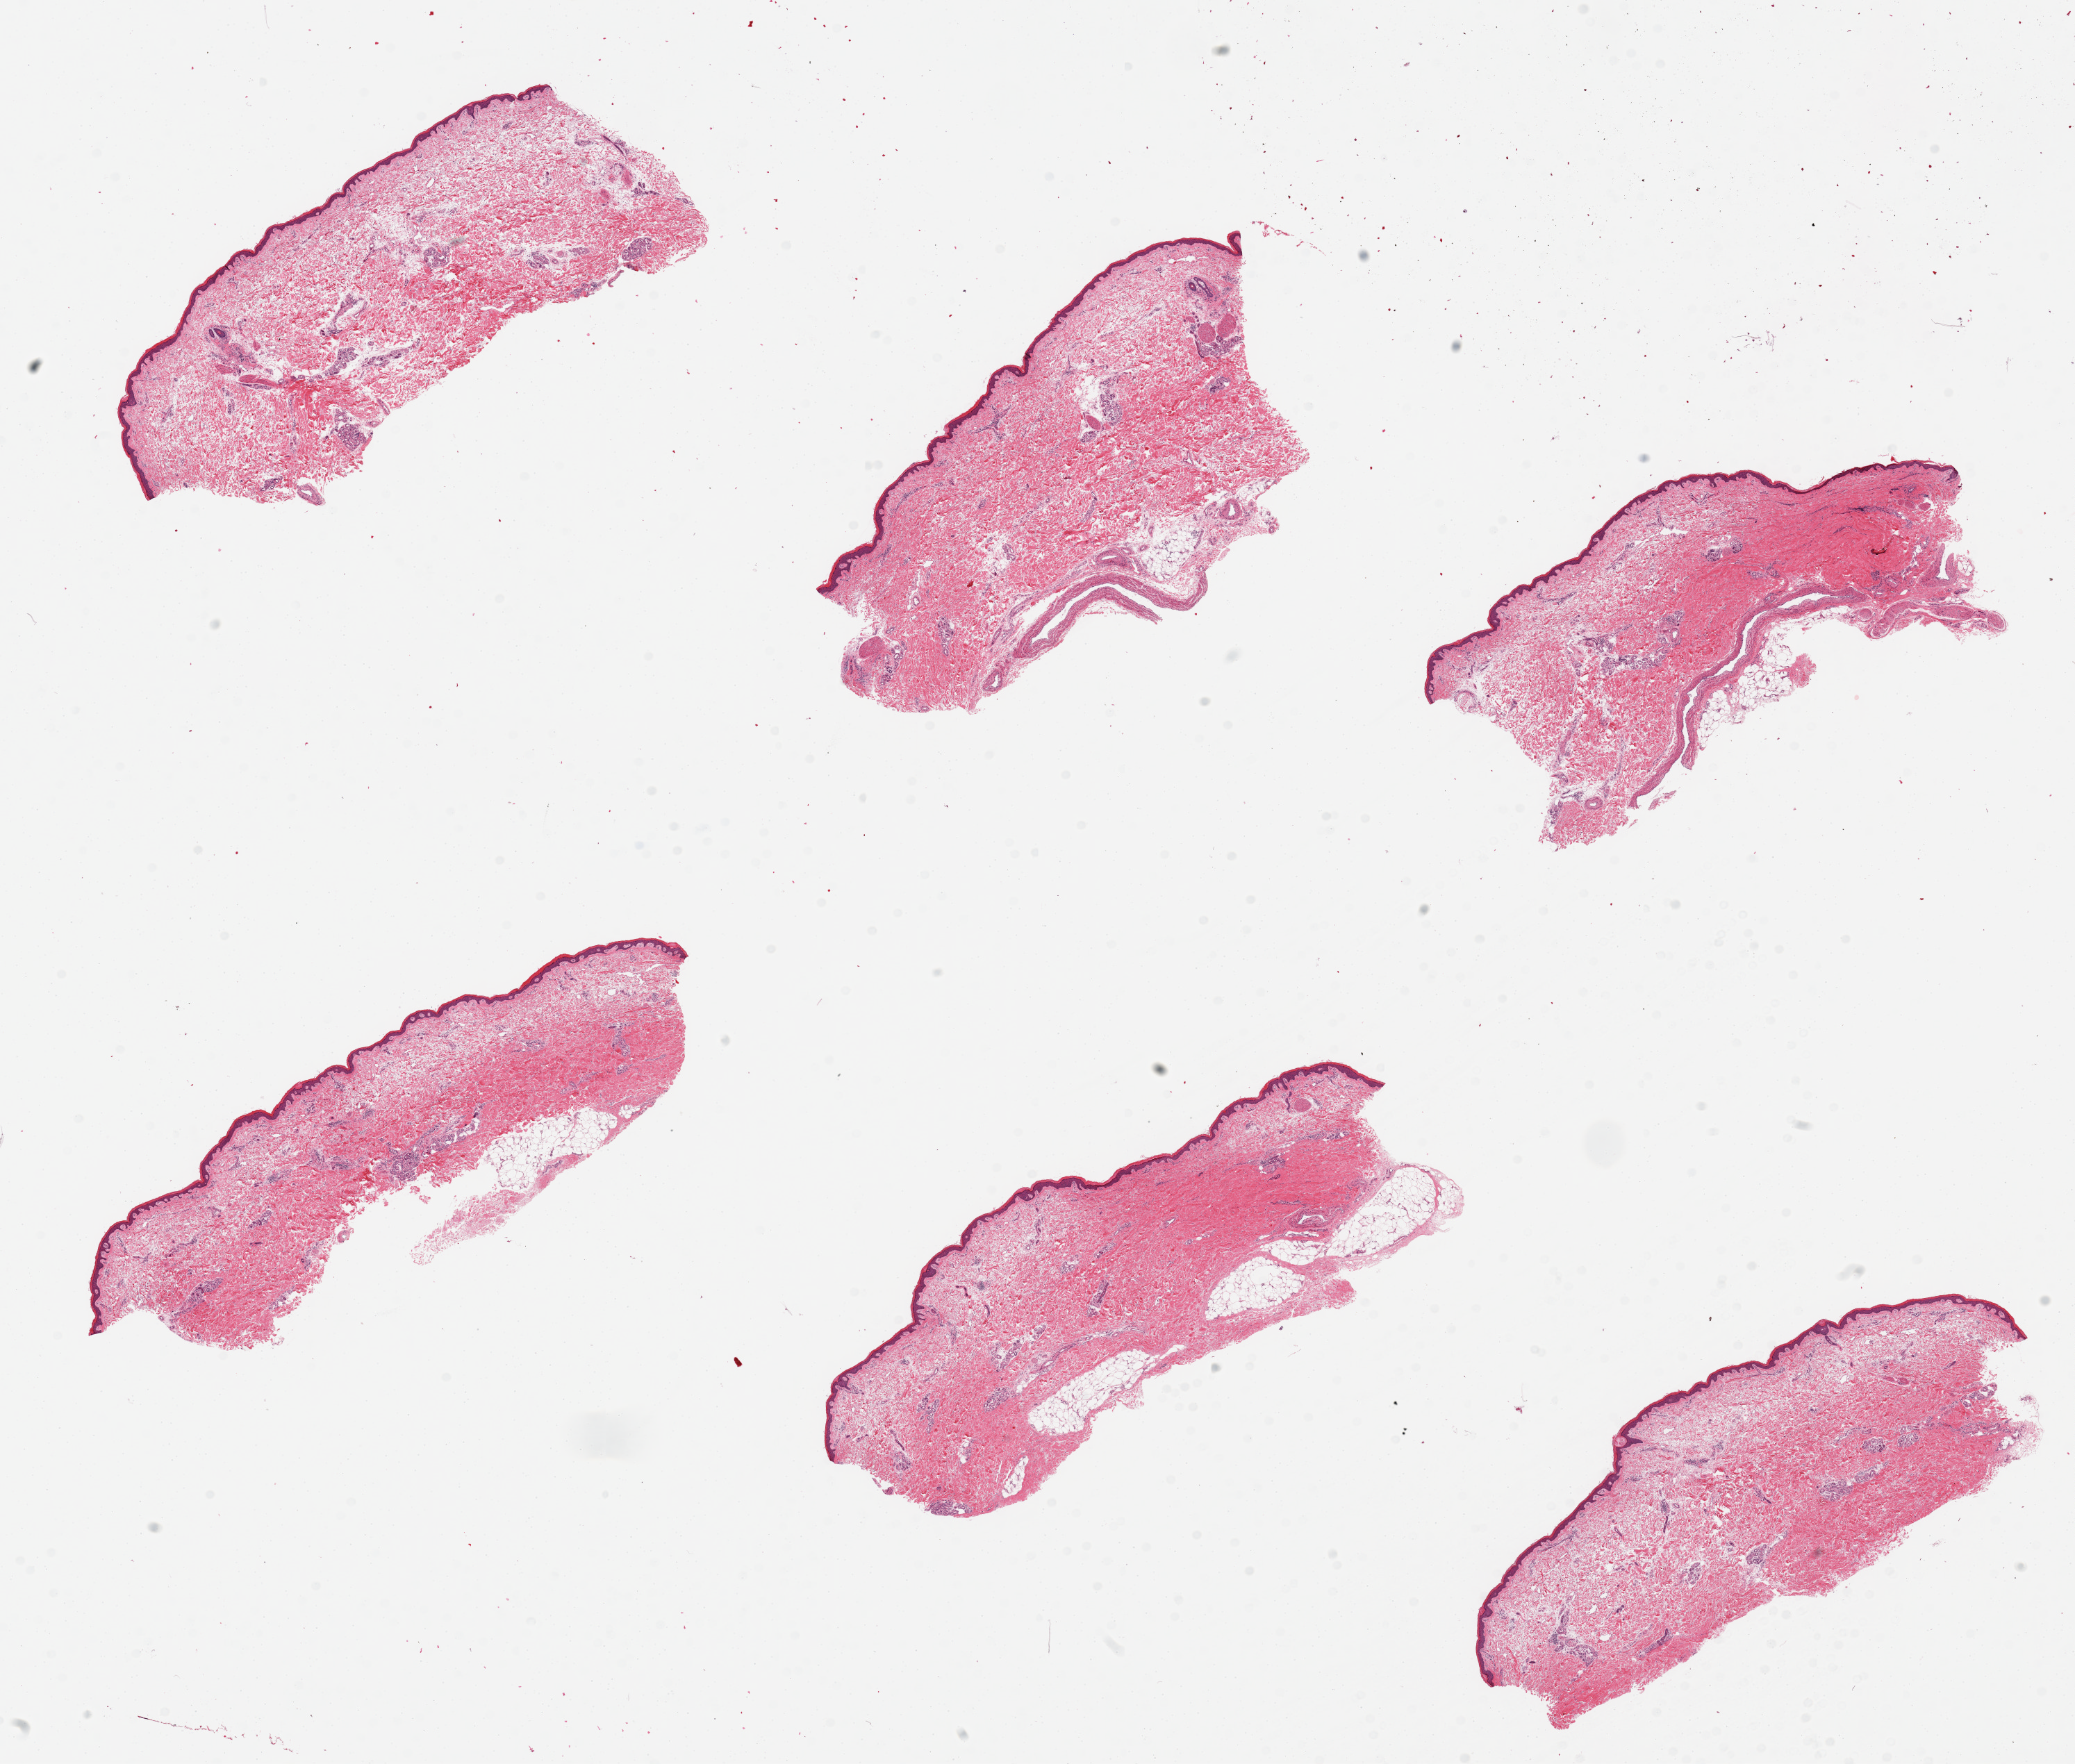
Haematoxylin and eosin whole-slide image, brightfield — low-resolution overview of the scanned area, about 23.6 x 20.1 mm; PAXgene-fixed paraffin-embedded (PFPE) section; section of skin of lower leg (target tissue); tissue donor sample. Donor: male.
- review note (as recorded): 6 pieces, 4 have up to 0.5 mm fat